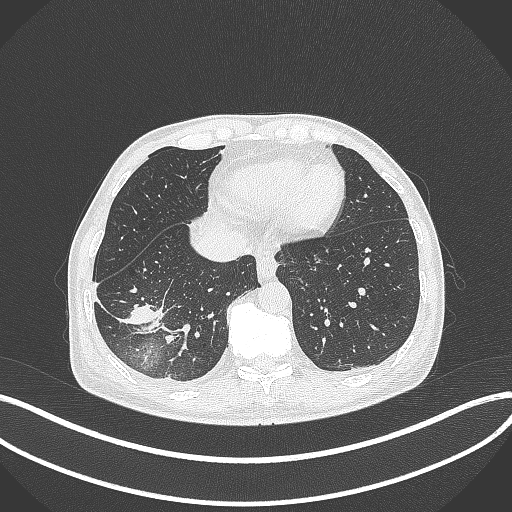
Chest CT, one axial slice. Position 99 of 388 along the scan axis. 120 kVp. Lung window (W 1500 / L -600 HU). 512 × 512 image matrix. Male patient, age 64 years. From the clinical record (not read from this slice): clinical TNM (as recorded): T3 N0 M0.
Structures marked on this image (bounding box drawn by a radiologist):
- lung tumour (recorded histology: adenocarcinoma): bounding box [x1, y1, x2, y2] px = [119, 296, 165, 339]